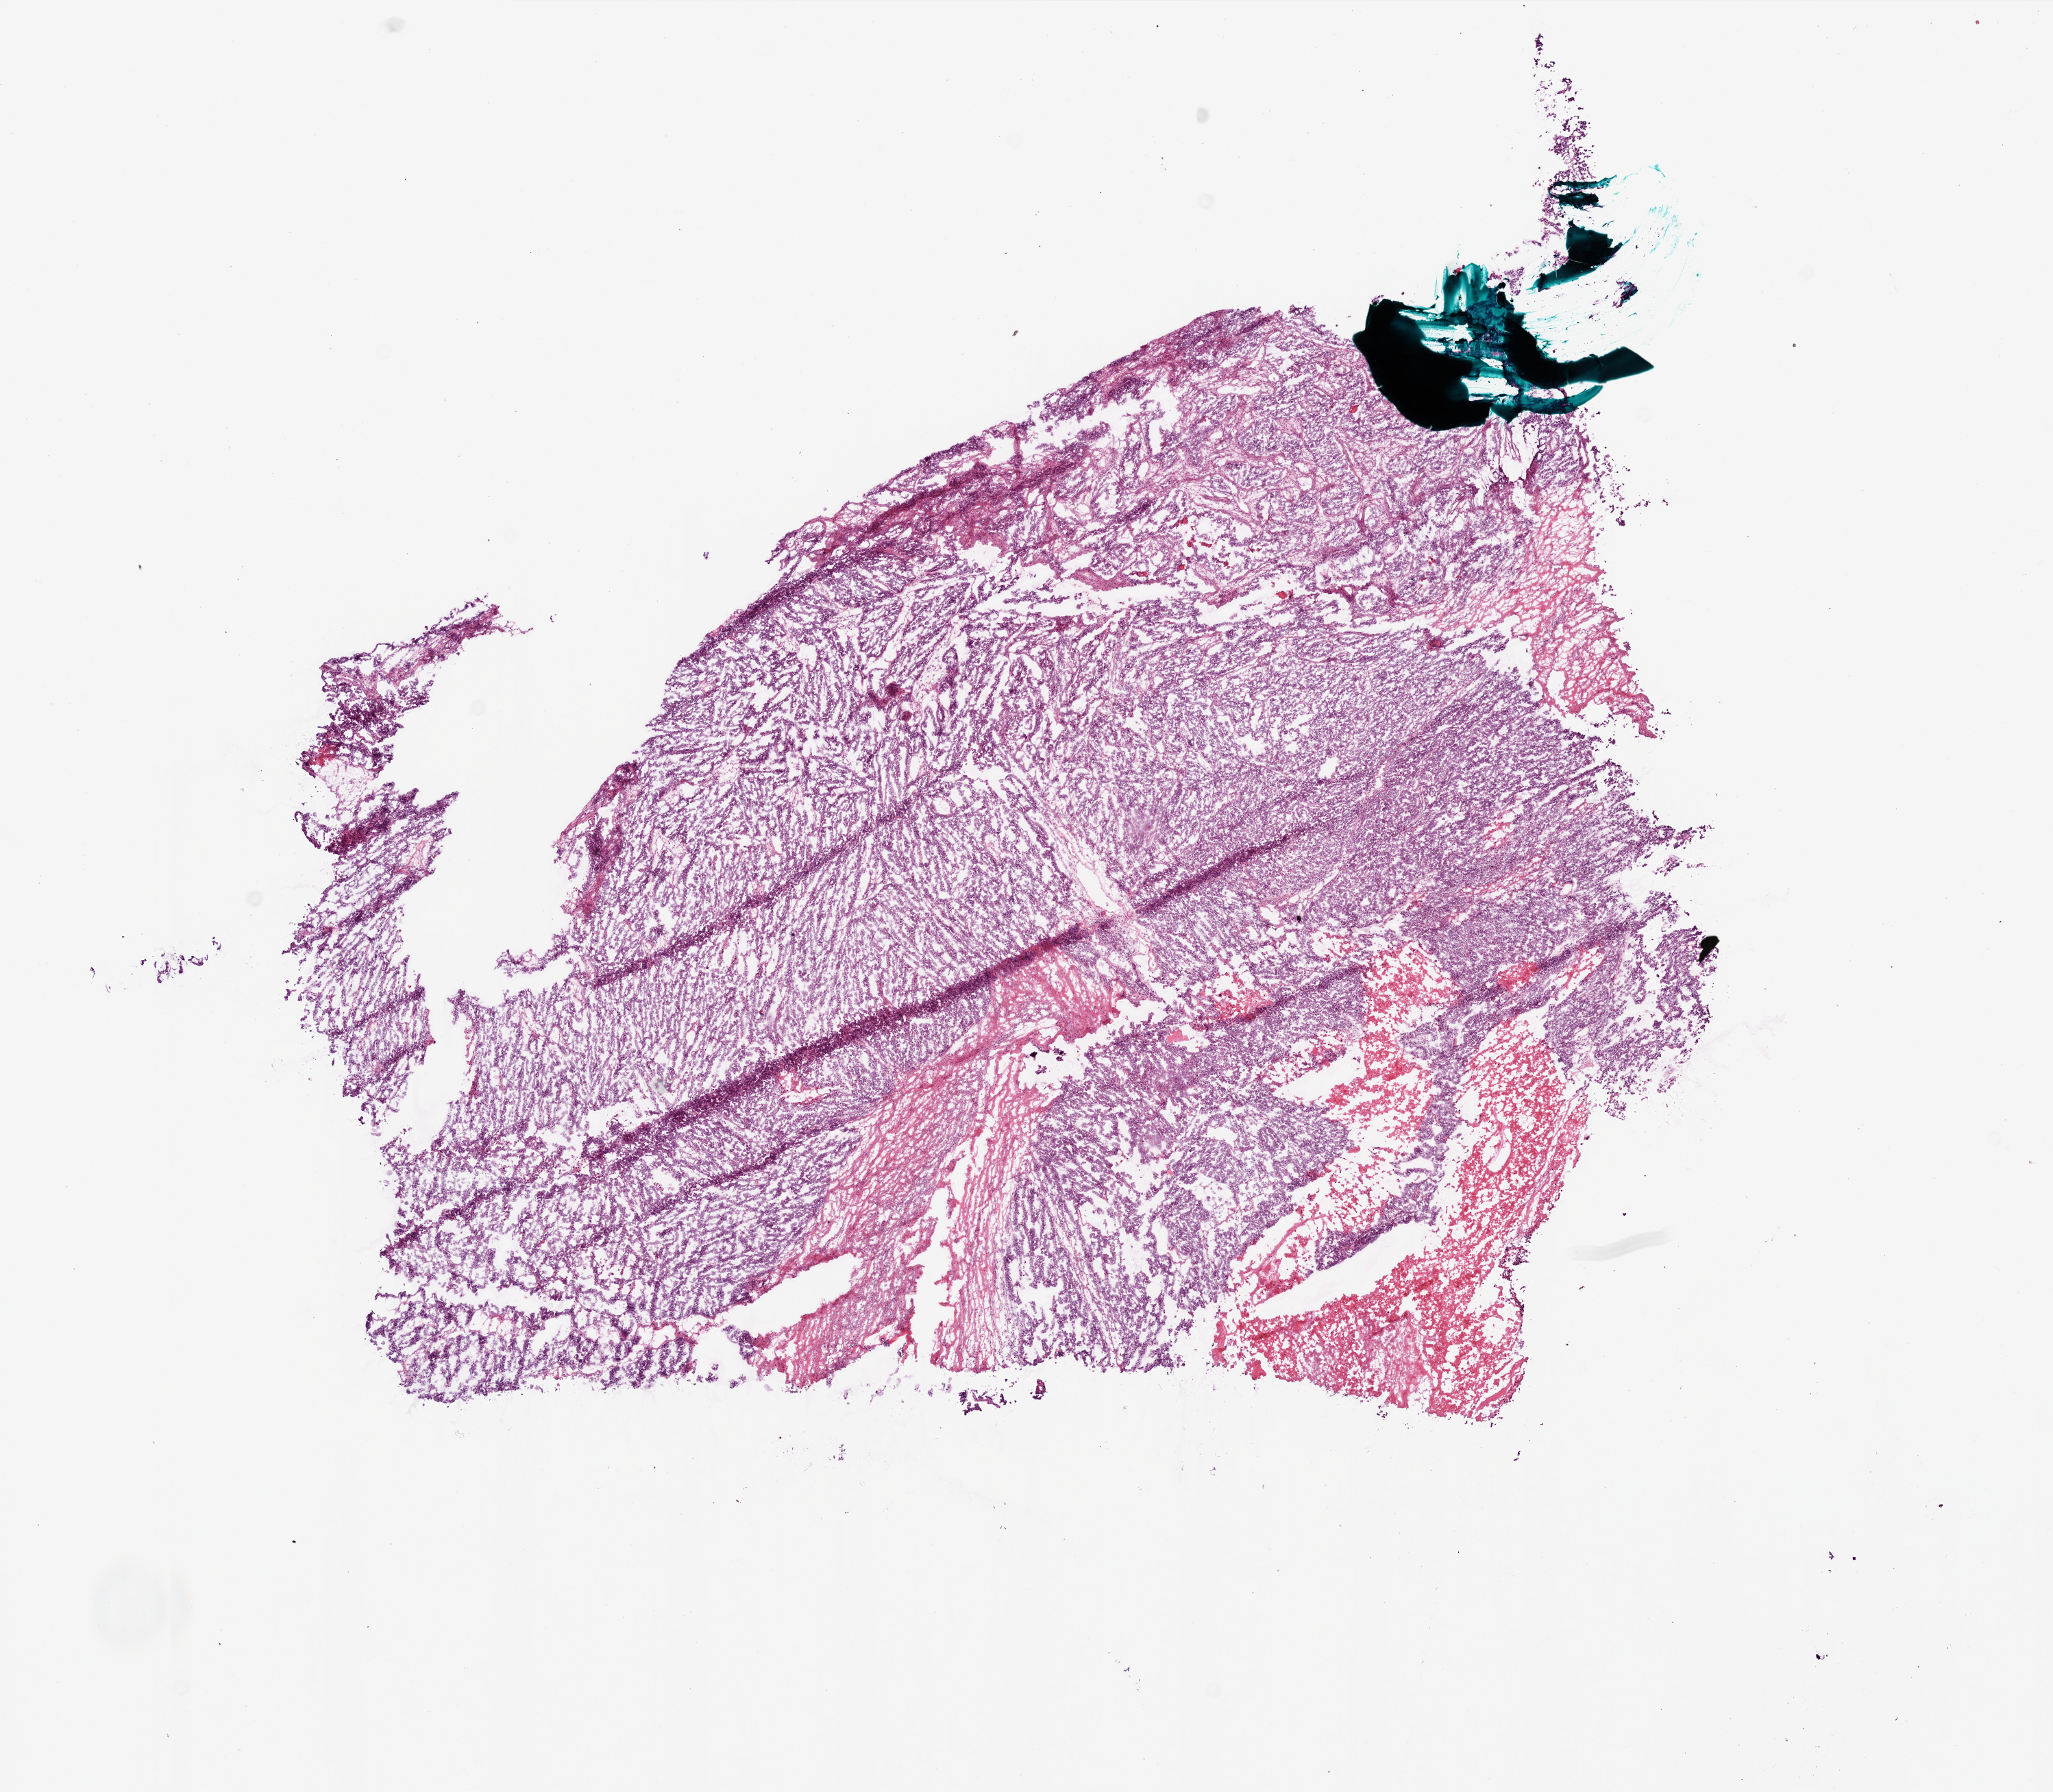
Whole-slide histology image, Hematoxylin and eosin (H&E) stained — whole scanned area (about 12.0 x 10.5 mm, from a 20x scan) shown as a low-resolution overview. Frozen section from the bottom of the tissue portion. Sample: primary tumour, ovary. Patient: female, age at initial diagnosis 65 years. Histologic grade: G3 (poorly differentiated). Composition of this section per pathologist review: tumour cells 80%, tumour nuclei 90%, normal cells 0%, stromal cells 20%, necrosis 0%.
Diagnosis: Serous cystadenocarcinoma, NOS. FIGO stage: IIIC.